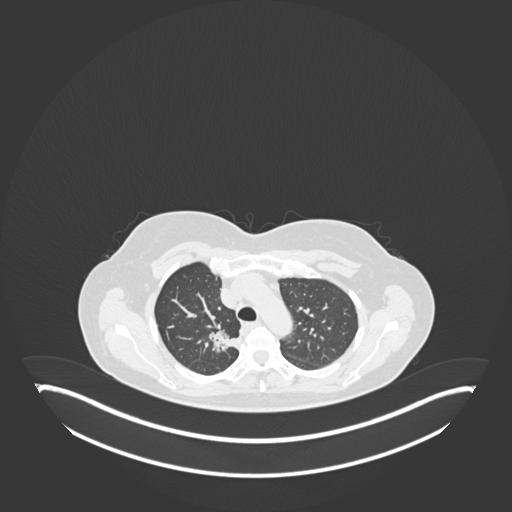
Chest CT, one axial slice; position 133 of 181 along the scan axis; reconstruction kernel B30f; 120 kVp; lung window (W 1500 / L -600 HU); 1 mm slice thickness; 512 × 512 image matrix. Female patient, age 65 years. Case-level facts recorded for this patient, not image findings: clinical TNM (as recorded): T1b N0 M0; histopathological grade: G2.
Outlined on this slice (bounding box drawn by a radiologist):
- lung tumour (recorded histology: adenocarcinoma): box from (x=208, y=328) to (x=241, y=355) px